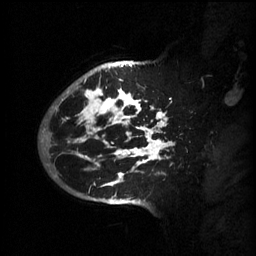
Breast MRI (dynamic contrast-enhanced), one sagittal slice. Position 45 of 60 along the scan axis. 3 images stored at this slice position (order not interpretable as contrast timing). 1.5 T. TE 4.2 ms, TR 11 ms. 2 mm slice thickness. 256 × 256 image matrix. Female patient, age 51 years.
Outlined on this slice (semi-automatically segmented with operator editing):
- analysis volume of interest (the breast-tissue region the enhancement analysis was run in; not a lesion): box from (x=63, y=80) to (x=175, y=201) px
- tumour enhancement mask (voxels above the 70 % enhancement threshold inside the analysis volume of interest): (x=63, y=80)–(x=175, y=187)